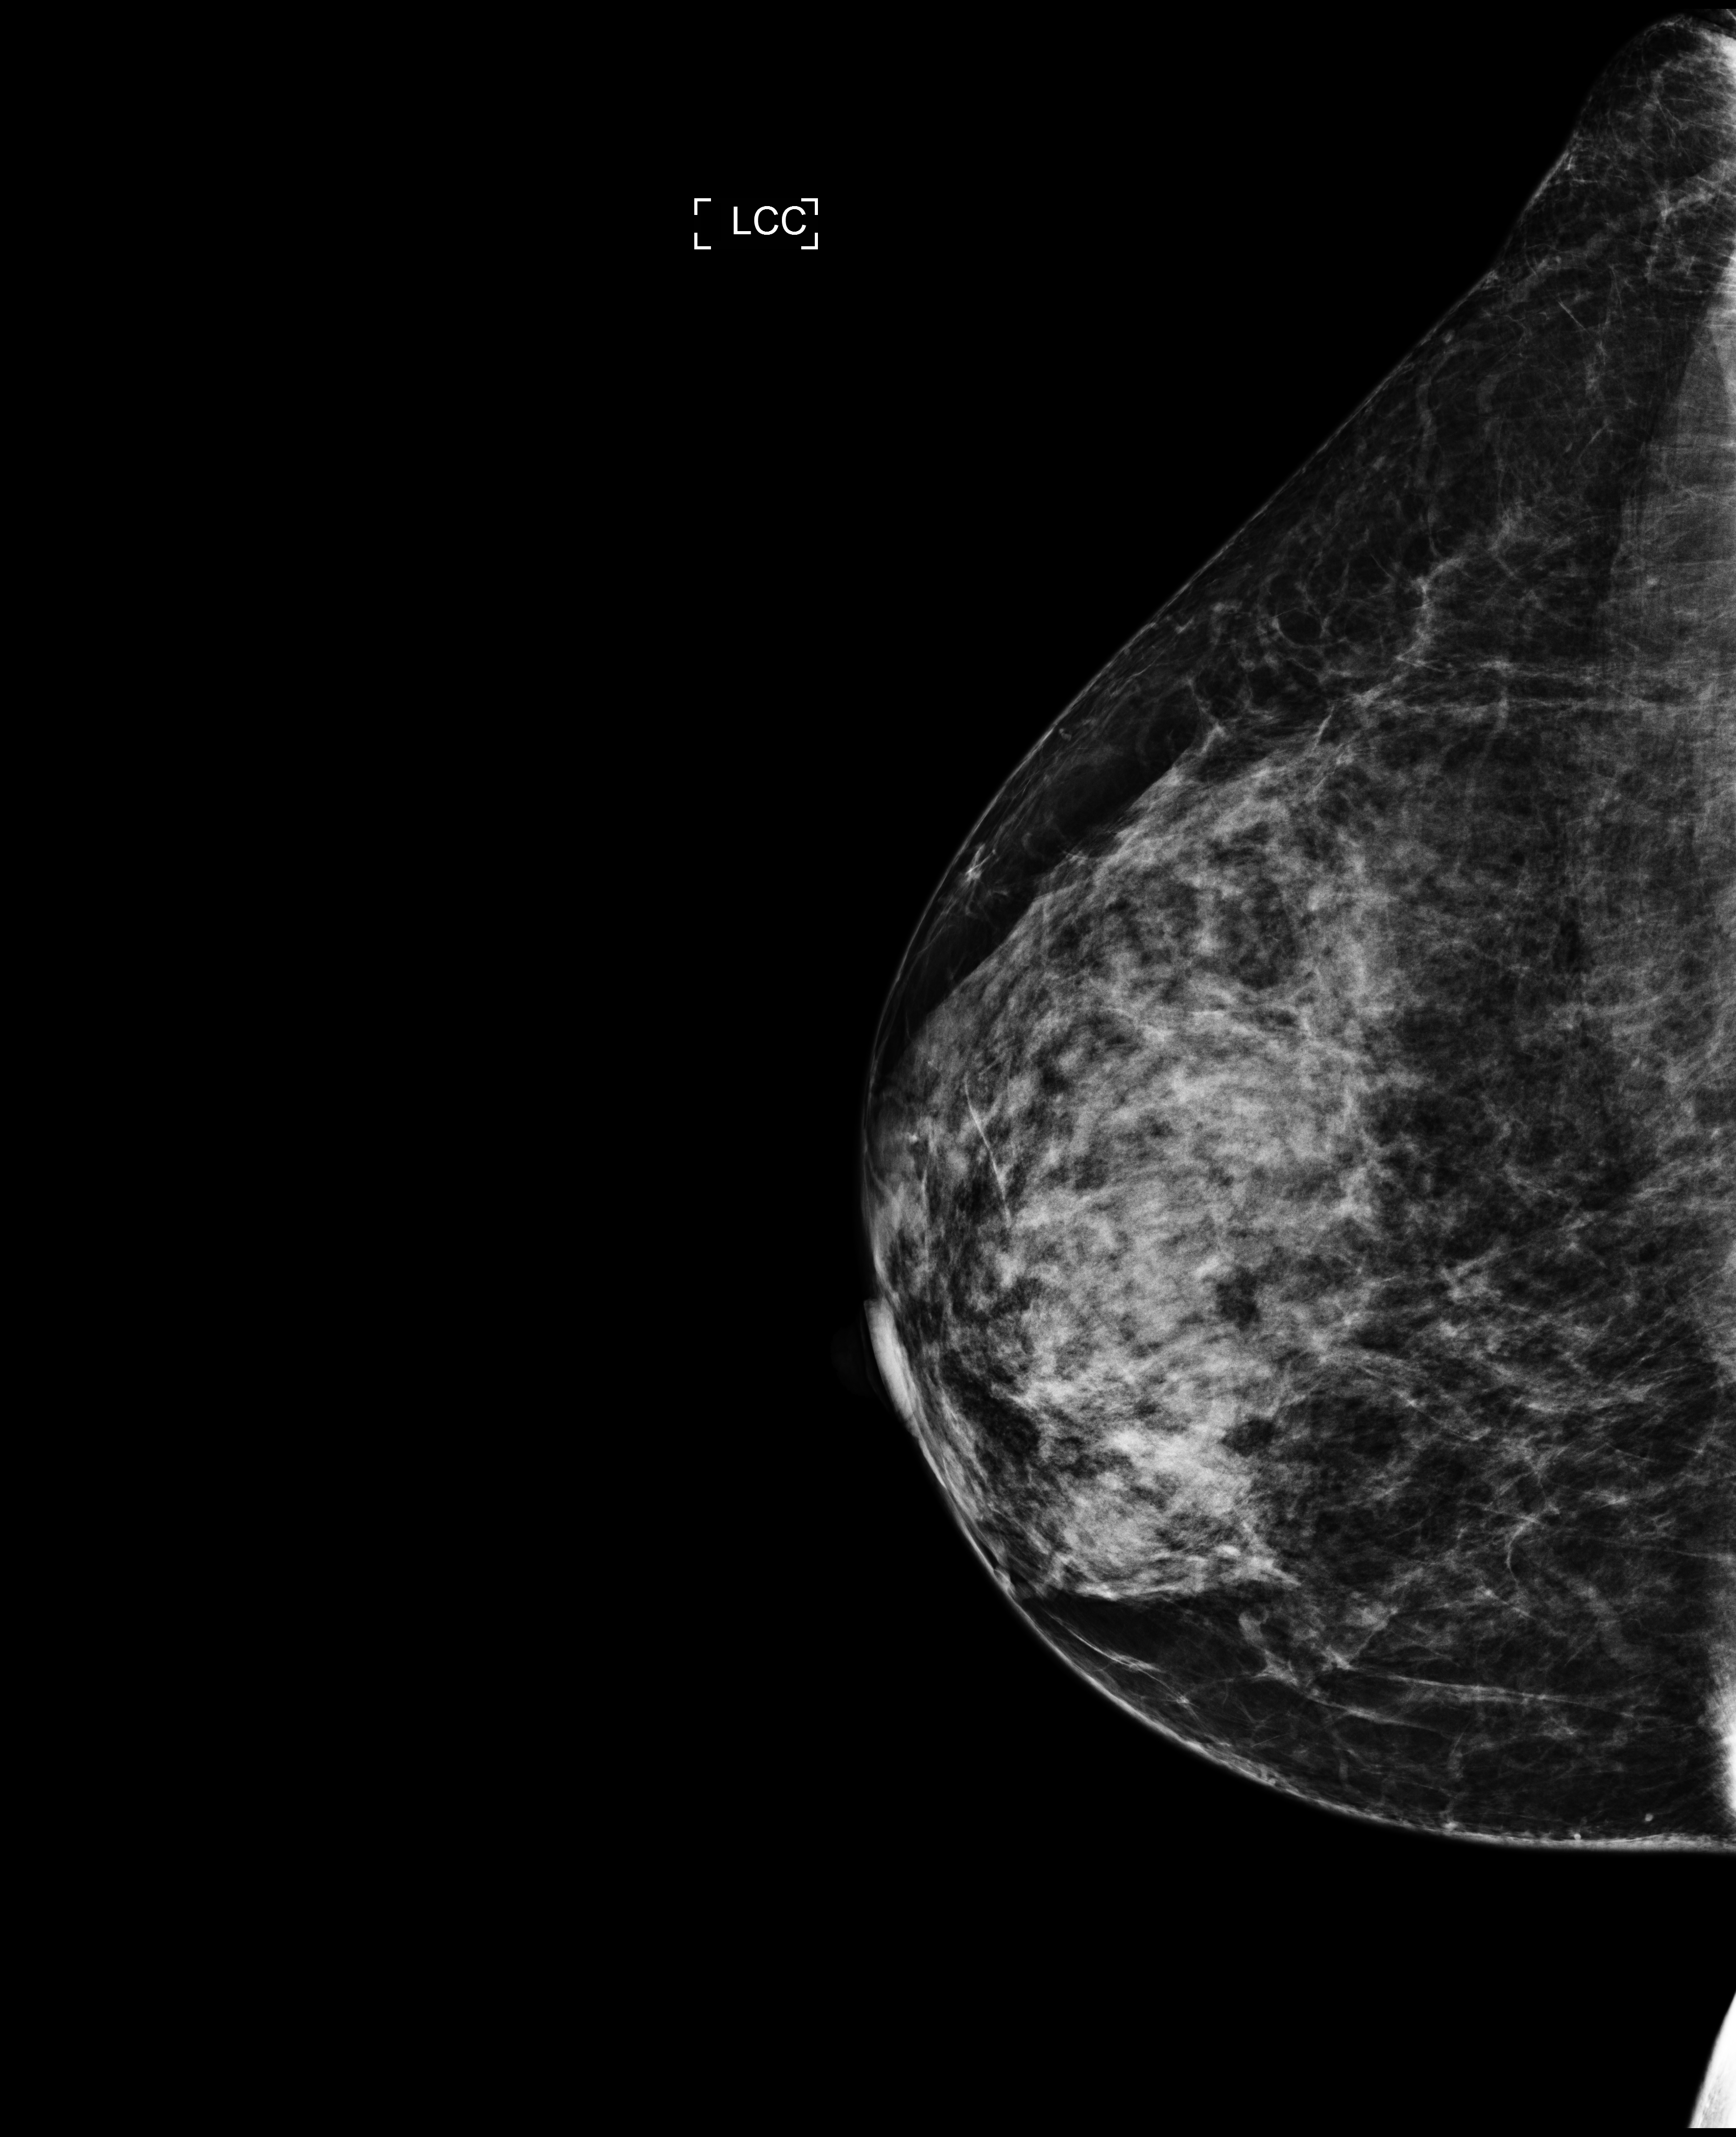
Annual screening mammography examination, compressed breast thickness 76 mm. Female patient, age 43 years.
Image type: full-field digital mammogram. Breast: left. Projection: CC view.